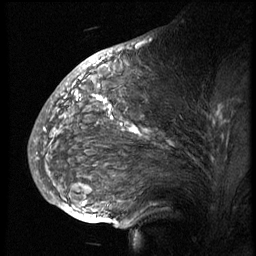
Breast MRI (dynamic contrast-enhanced), one sagittal slice. Slice 38 of 74 in the series (ordered by position). 3 images stored at this slice position (order not interpretable as contrast timing). 1.5 T. TE 4.2 ms, TR 8.9 ms. 2.5 mm slice thickness. 256 × 256 image matrix. Female patient, age 57 years. Case-level facts recorded for this patient, not image findings: setting: breast cancer imaged before/during neoadjuvant chemotherapy; receptor status: HER2-positive.
Outlined on this slice (semi-automatic segmentation, software-assisted and operator-edited):
- analysis volume of interest (the breast-tissue region the enhancement analysis was run in; not a lesion): box from (x=51, y=67) to (x=248, y=173) px
- tumour enhancement mask (voxels above the 140 % enhancement threshold inside the analysis volume of interest): (x=98, y=97)–(x=223, y=136)